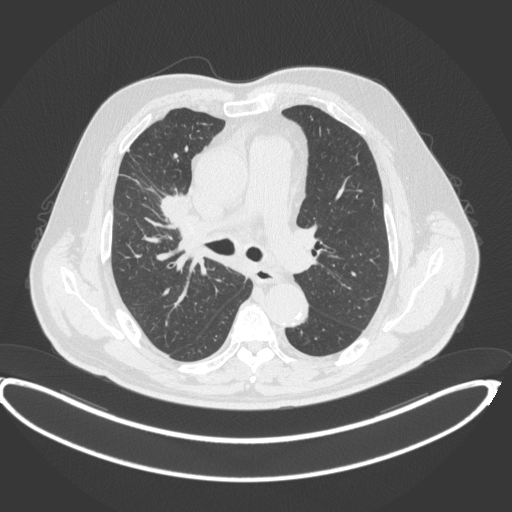
Chest CT, one axial slice; reconstruction kernel B31f; lung window (W 1500 / L -600 HU); 512 × 512 image matrix, field of view 448 × 448 mm. Patient: male, 62 years. Case-level facts recorded for this patient, not image findings: clinical TNM (as recorded): T1c N3 M1c.
Annotated regions visible in this slice (bounding box drawn by a radiologist):
- lung tumour (recorded histology: adenocarcinoma): bounding box [x1, y1, x2, y2] px = [156, 184, 194, 221]